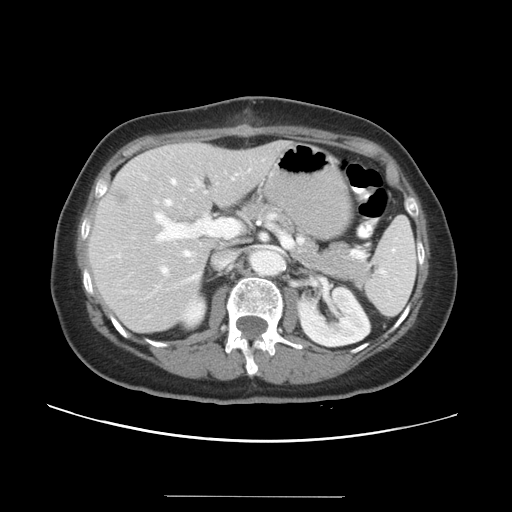
Contrast-enhanced abdominal CT, one axial slice; intravenous contrast given; soft-tissue window (W 400 / L 40 HU); 5 mm slice thickness; 512 × 512 image matrix, field of view 382 × 382 mm. Female patient, age 69 years. From the clinical record (not read from this slice): diagnosis: colorectal cancer liver metastases, imaged before liver resection; multiple liver metastases: yes; largest metastasis: 1.4 cm; disease in both lobes: yes.
Structures marked on this image (manually delineated by an expert):
- hepatic veins: bounding box <155,179,199,282> (left, top, right, bottom; pixels)
- liver: <90,141,290,332>
- planned liver remnant (the part of the liver to remain after resection): <90,141,289,332>
- portal vein (with intrahepatic branches): <155,212,365,274>
- liver metastasis: <108,186,128,206>